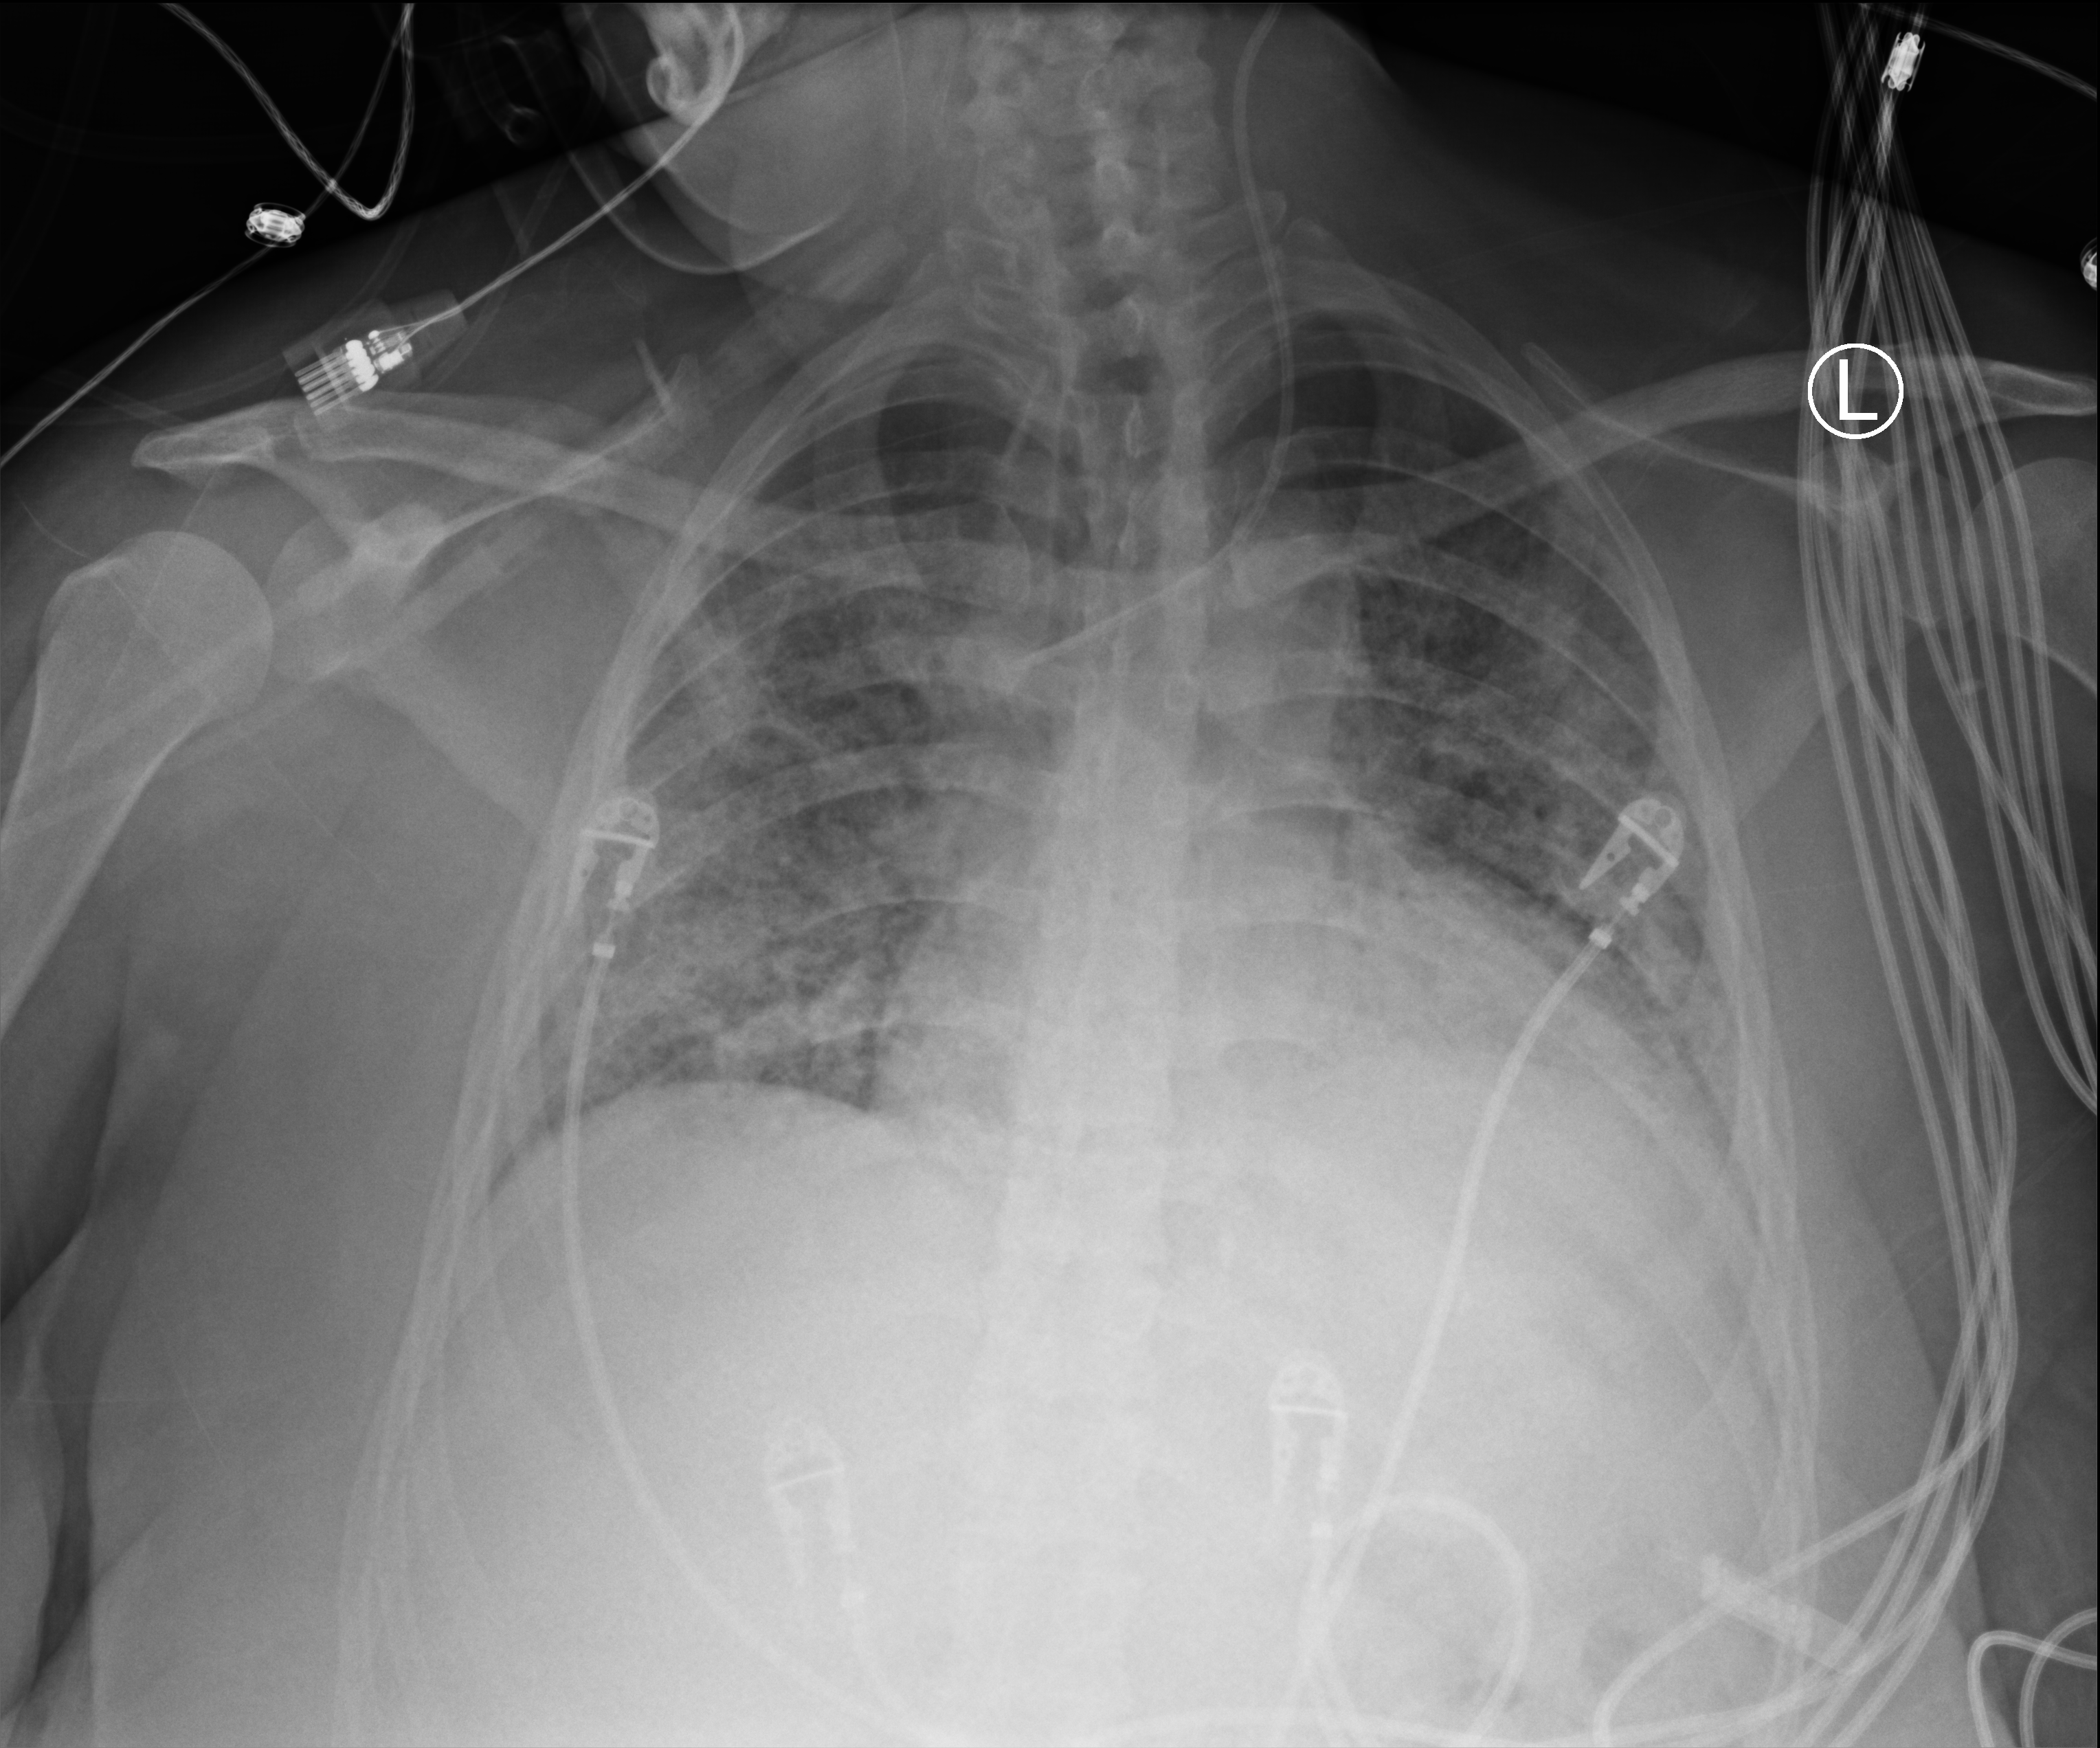
Chest X-ray (portable); anteroposterior (AP) projection. Female patient hospitalised with COVID-19, age 18–59 years.
Admission-level facts for this patient (not findings on this image; timing relative to this image not recorded): admitted to intensive care during this hospital stay: no.